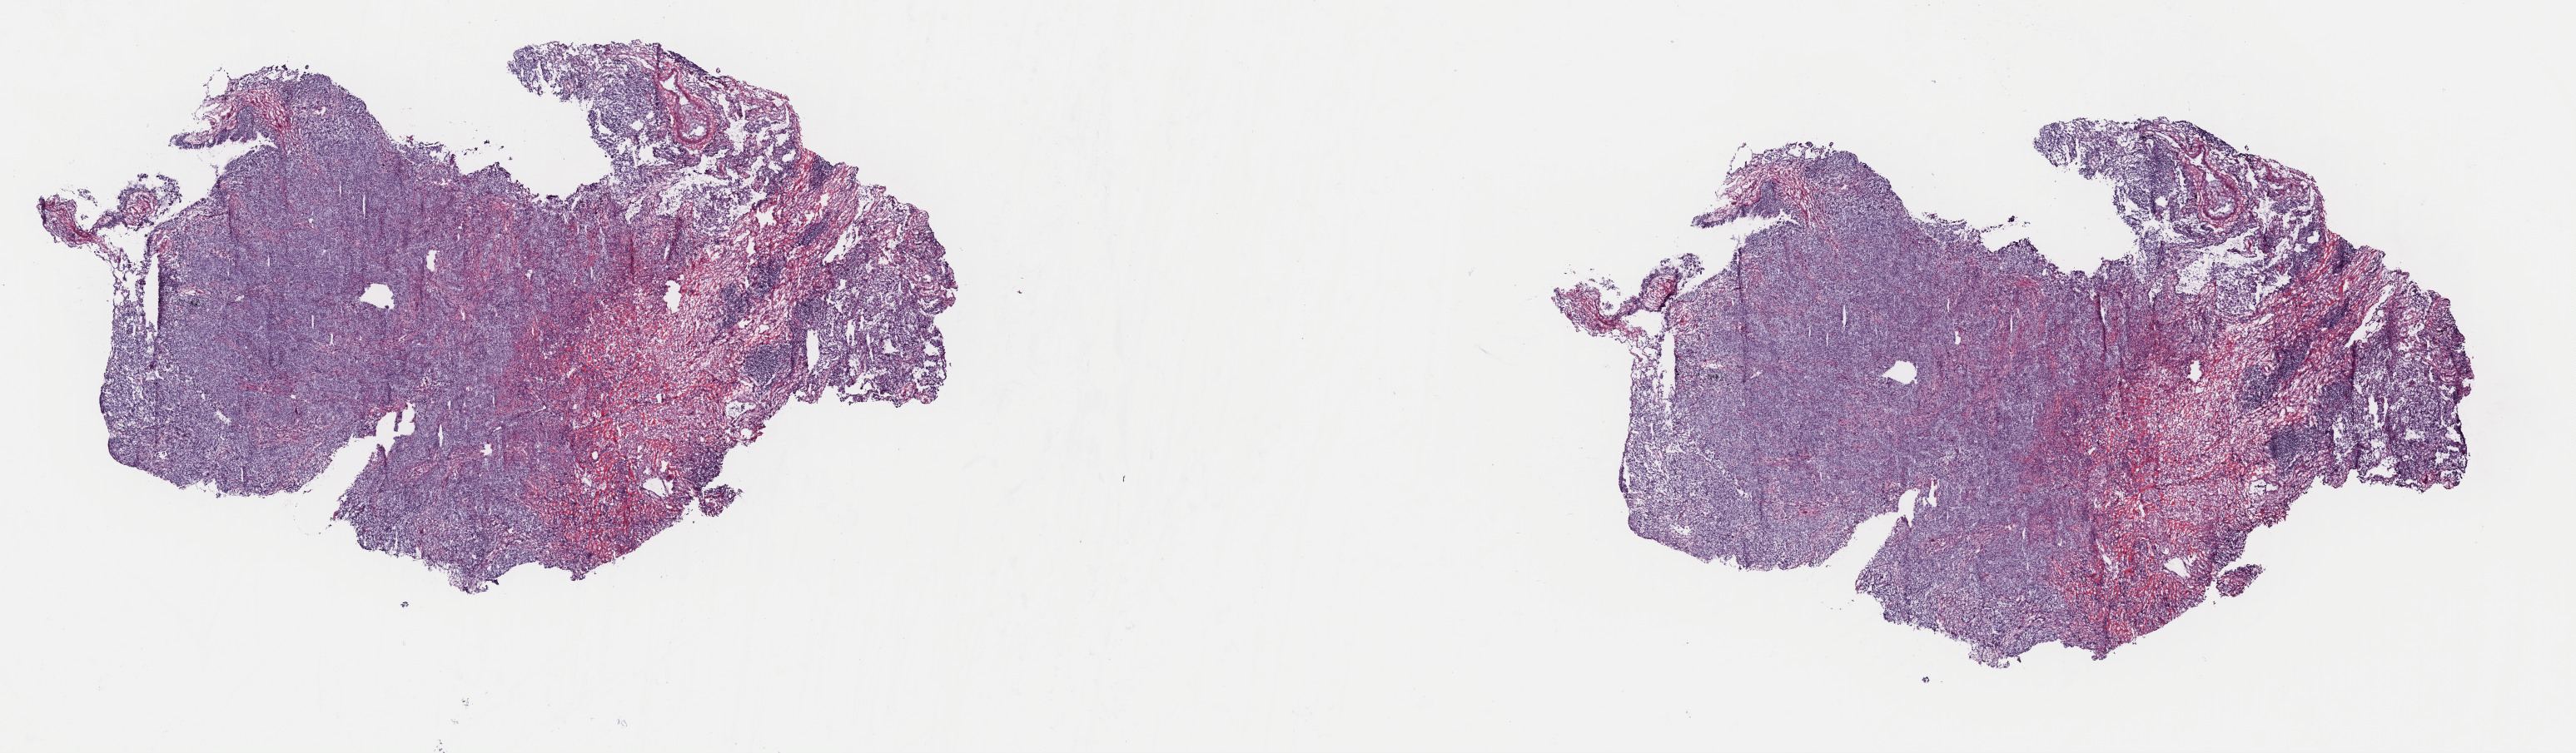
H&E-stained whole-slide image, shown as a low-resolution overview of the whole scanned area (about 24.4 x 7.1 mm, slide scanned at 40x). Frozen section from the top of the tissue portion. Primary tumour sample from the lung. Male patient; age at initial diagnosis 81 years. Pathologist review of this section (percent, as recorded): tumour cells 100%, tumour nuclei 65%, normal cells 0%, stromal cells 0%, necrosis 0%. Infiltration values recorded for this section: lymphocyte infiltration 15%, monocyte infiltration 2%, neutrophil infiltration 0%.
TNM: T2a N0 M0. Histologic diagnosis: Adenocarcinoma with mixed subtypes (upper lobe, lung). AJCC pathologic stage: IB.